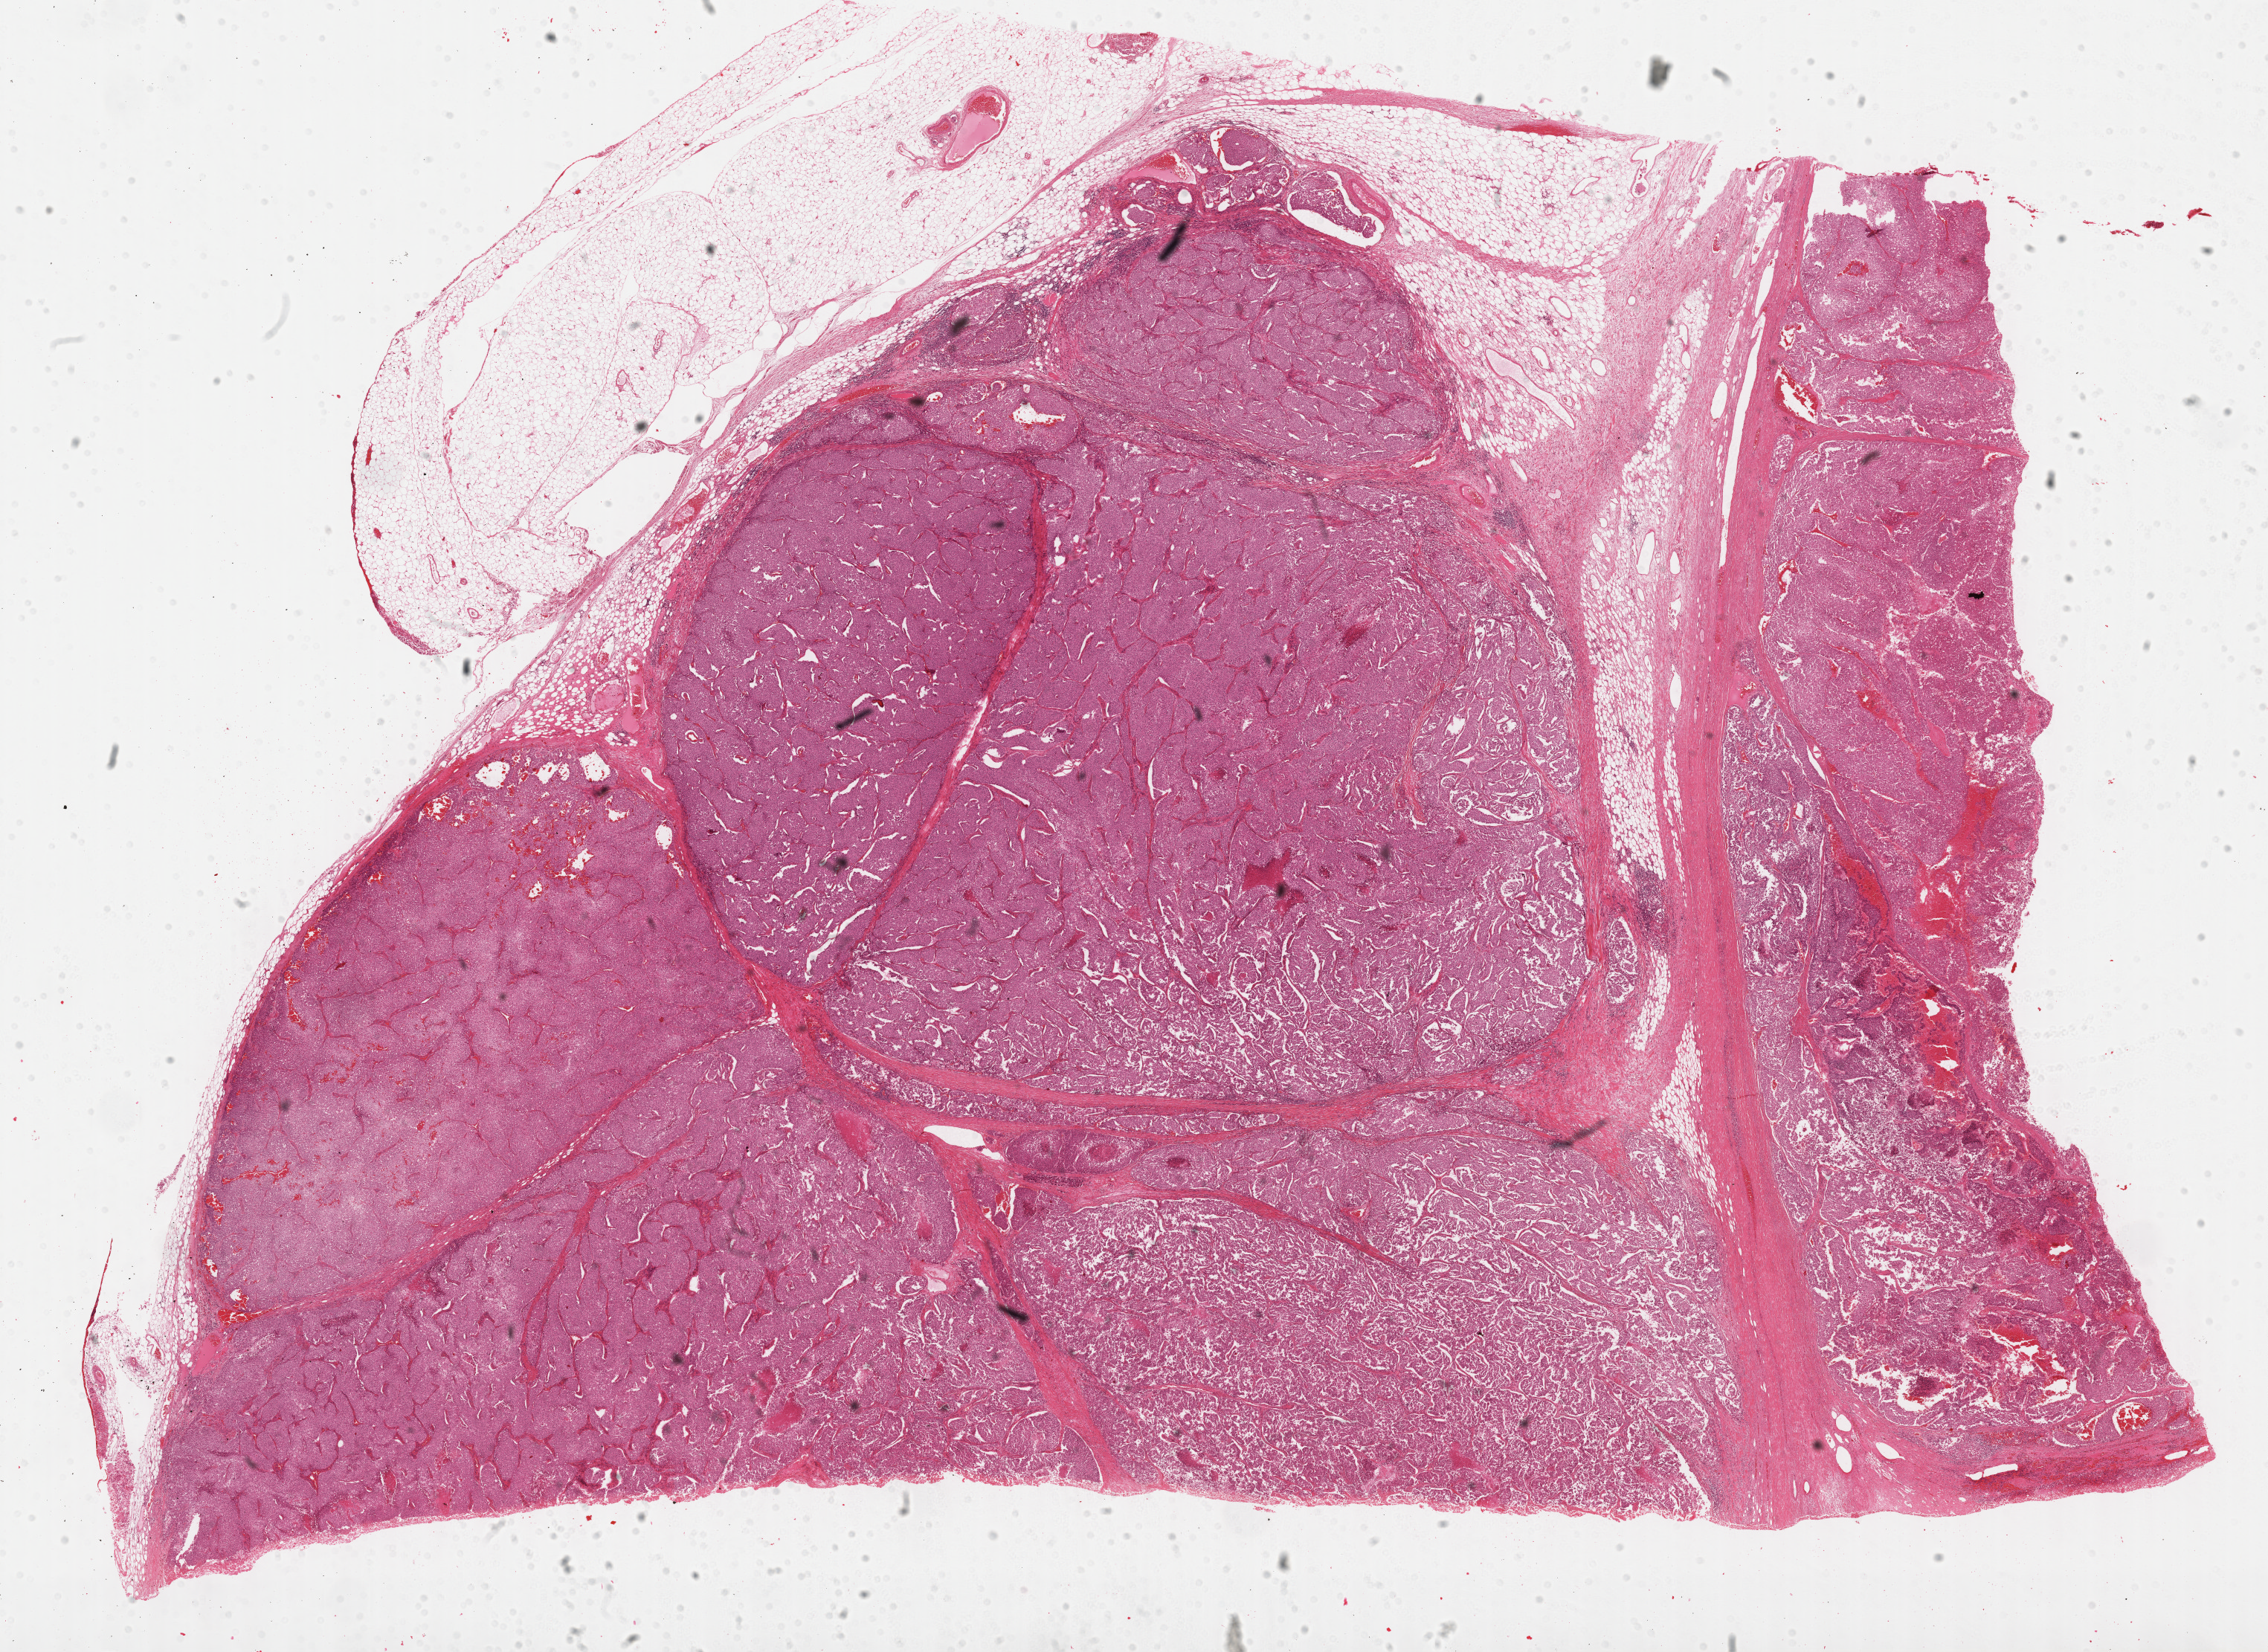
Digitized H&E tissue section (whole slide), low-resolution overview of the scanned area, about 24.7 x 18.0 mm (slide scanned at 40x). Formalin-fixed paraffin-embedded (FFPE) diagnostic section. Adrenal cortex, primary tumour sample. Male, age 65 years at initial diagnosis.
Pathologic diagnosis: Adrenal cortical carcinoma (cortex of adrenal gland).